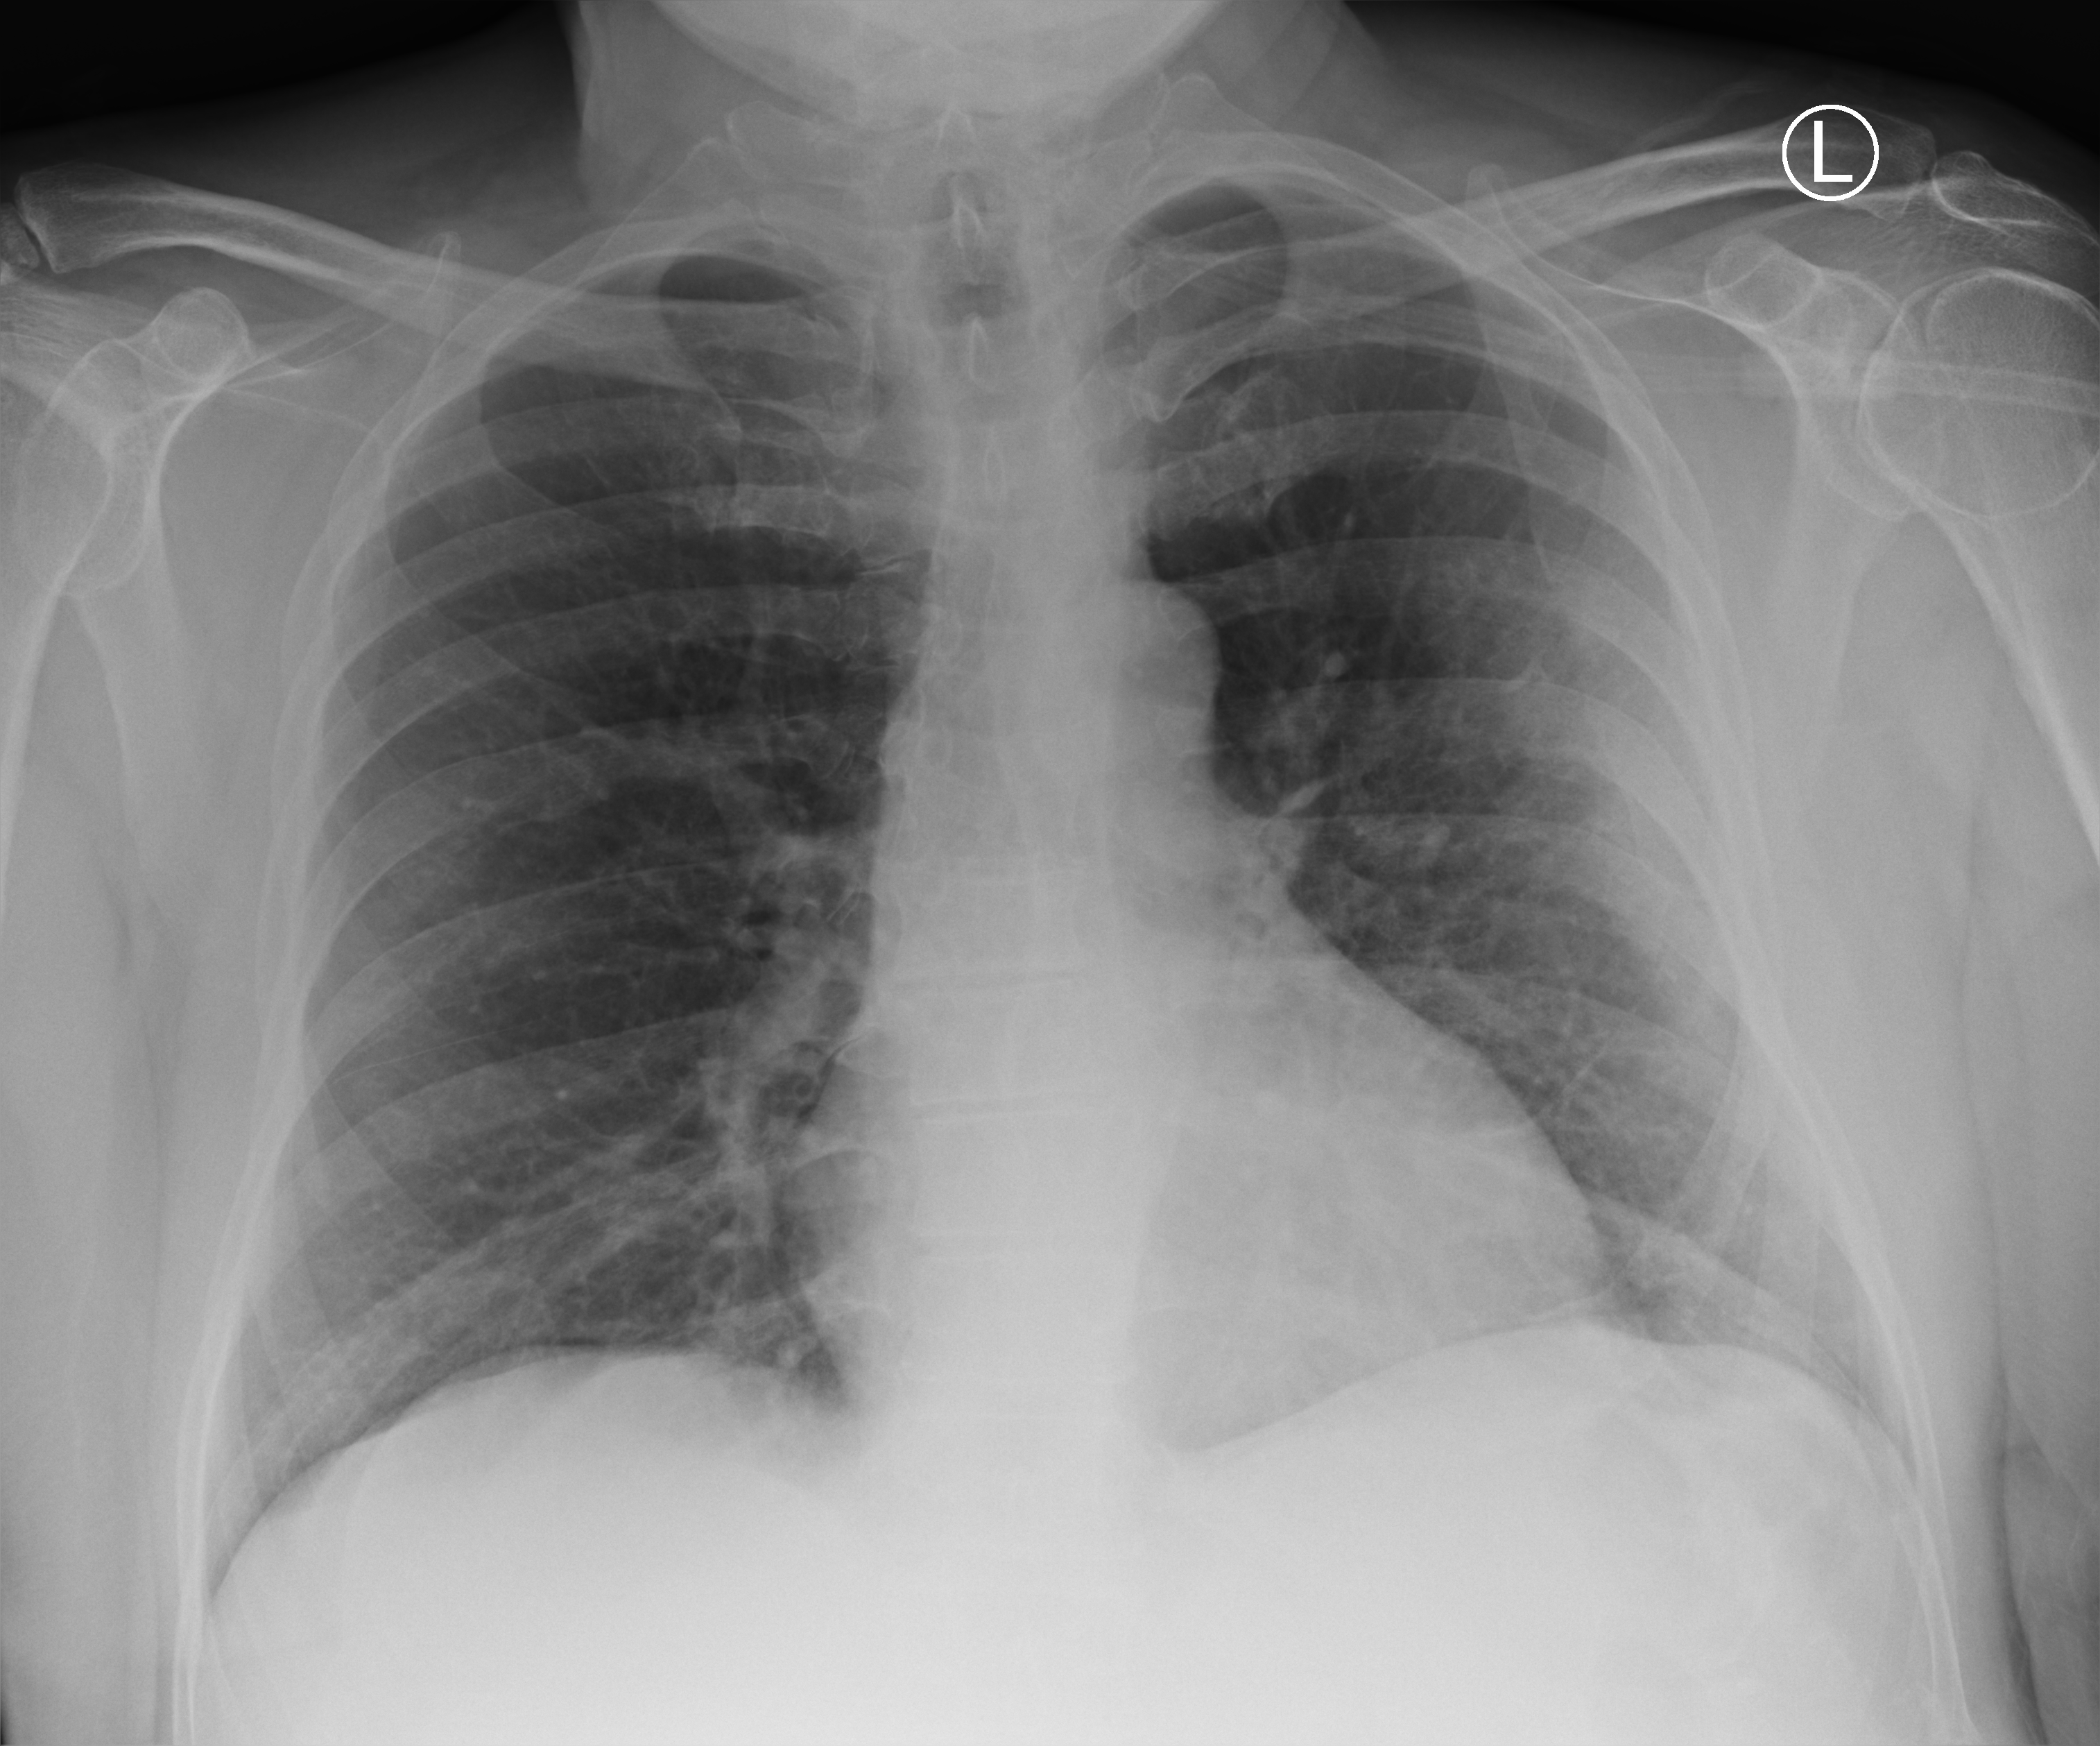
Portable chest radiograph, anteroposterior (AP) projection. Male patient hospitalised with COVID-19, age 60–74 years.
Admission-level facts for this patient (not findings on this image; timing relative to this image not recorded): admitted to intensive care during this hospital stay: no; mechanically ventilated during this hospital stay: no; other chronic lung disease (admission record): no.